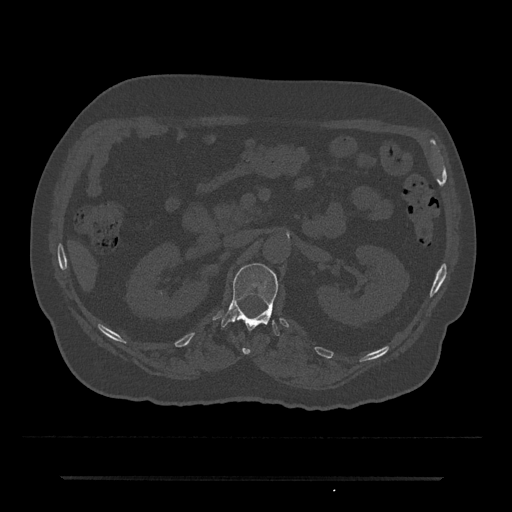
CT including the spine, one axial slice; slice 75 of 797 in the series (ordered by position); reconstruction kernel Br40s/3; 120 kVp; bone window (W 1800 / L 400 HU); 0.5 mm slice thickness; 512 × 512 image matrix, field of view 437 × 437 mm. Patient: male, 69 years. Case-level facts recorded for this patient, not image findings: primary cancer: prostate.
Structures marked on this image (semi-automatic segmentation, software-assisted and operator-edited):
- L1 vertebra: bounding box (x1, y1, x2, y2) in pixels: (221, 263, 280, 336)
- T12 vertebra: (242, 348, 251, 355)